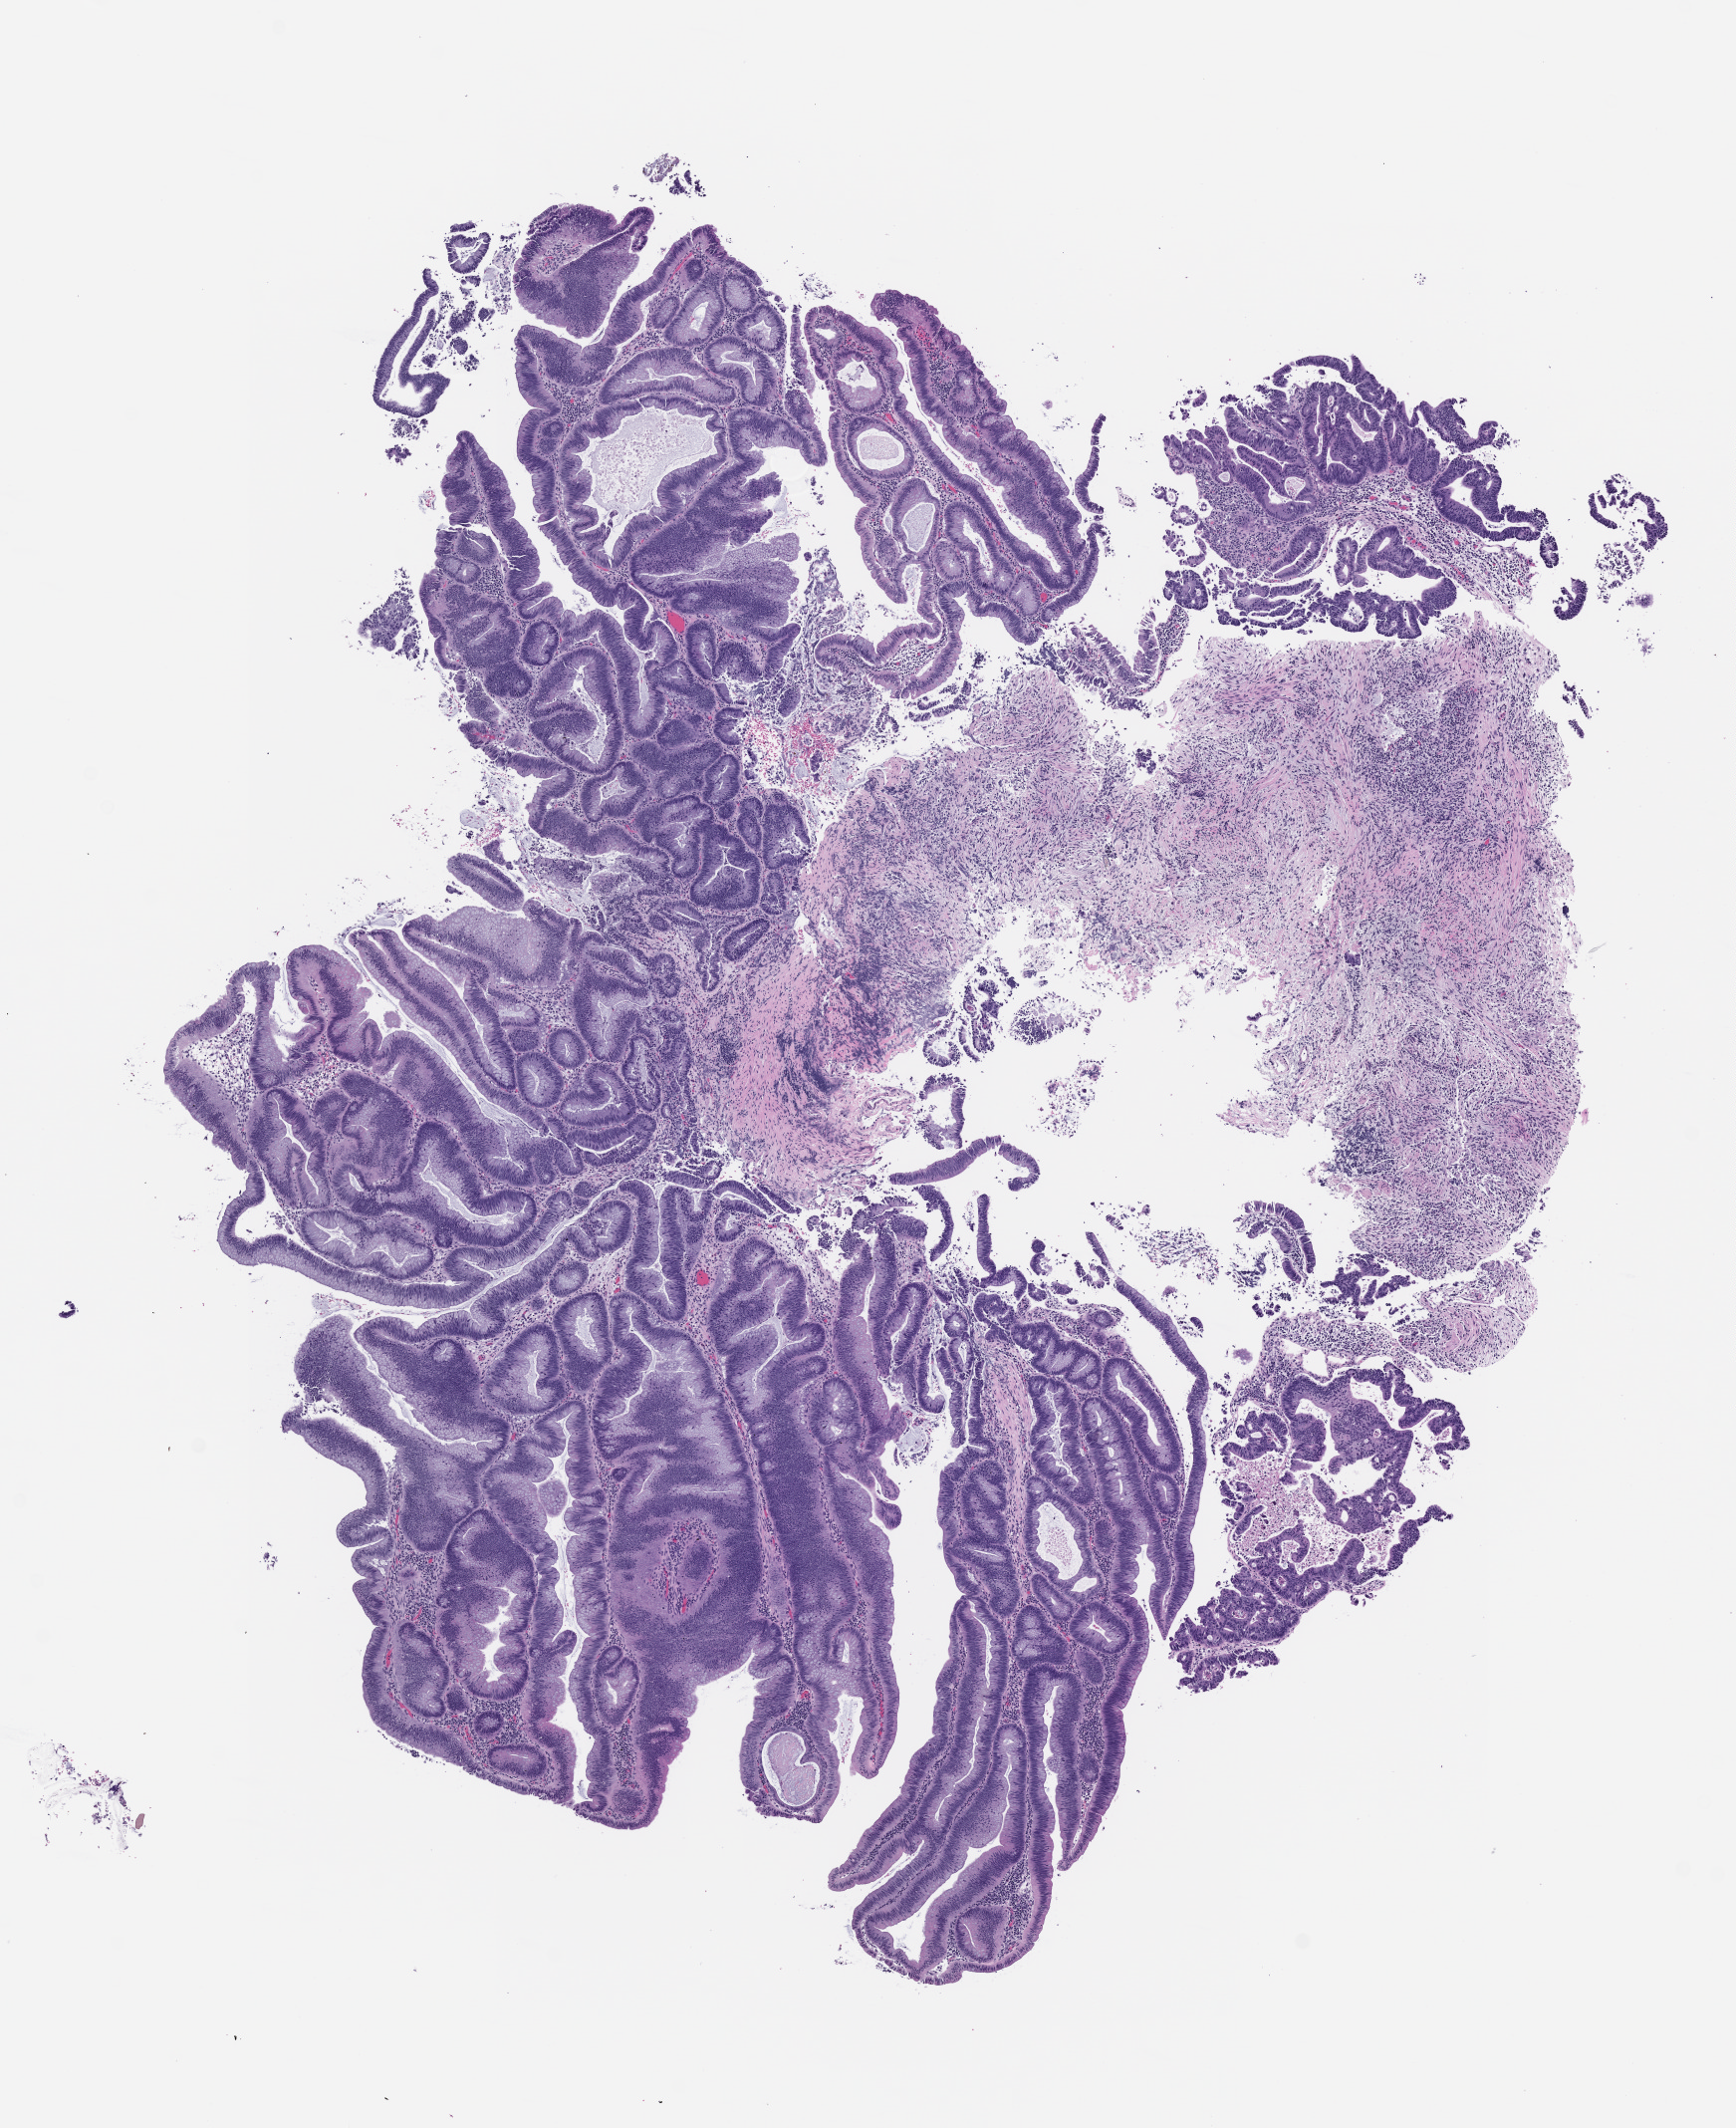
Digitized hematoxylin and eosin (H&E)-stained section of the patient's (originator) tumor tissue — shown as a low-resolution overview of the whole scanned area (about 7.0 x 8.6 mm). FFPE section. Originating tumor site category: rectum. Patient: female.
Diagnosis: Rectal Adenocarcinoma.